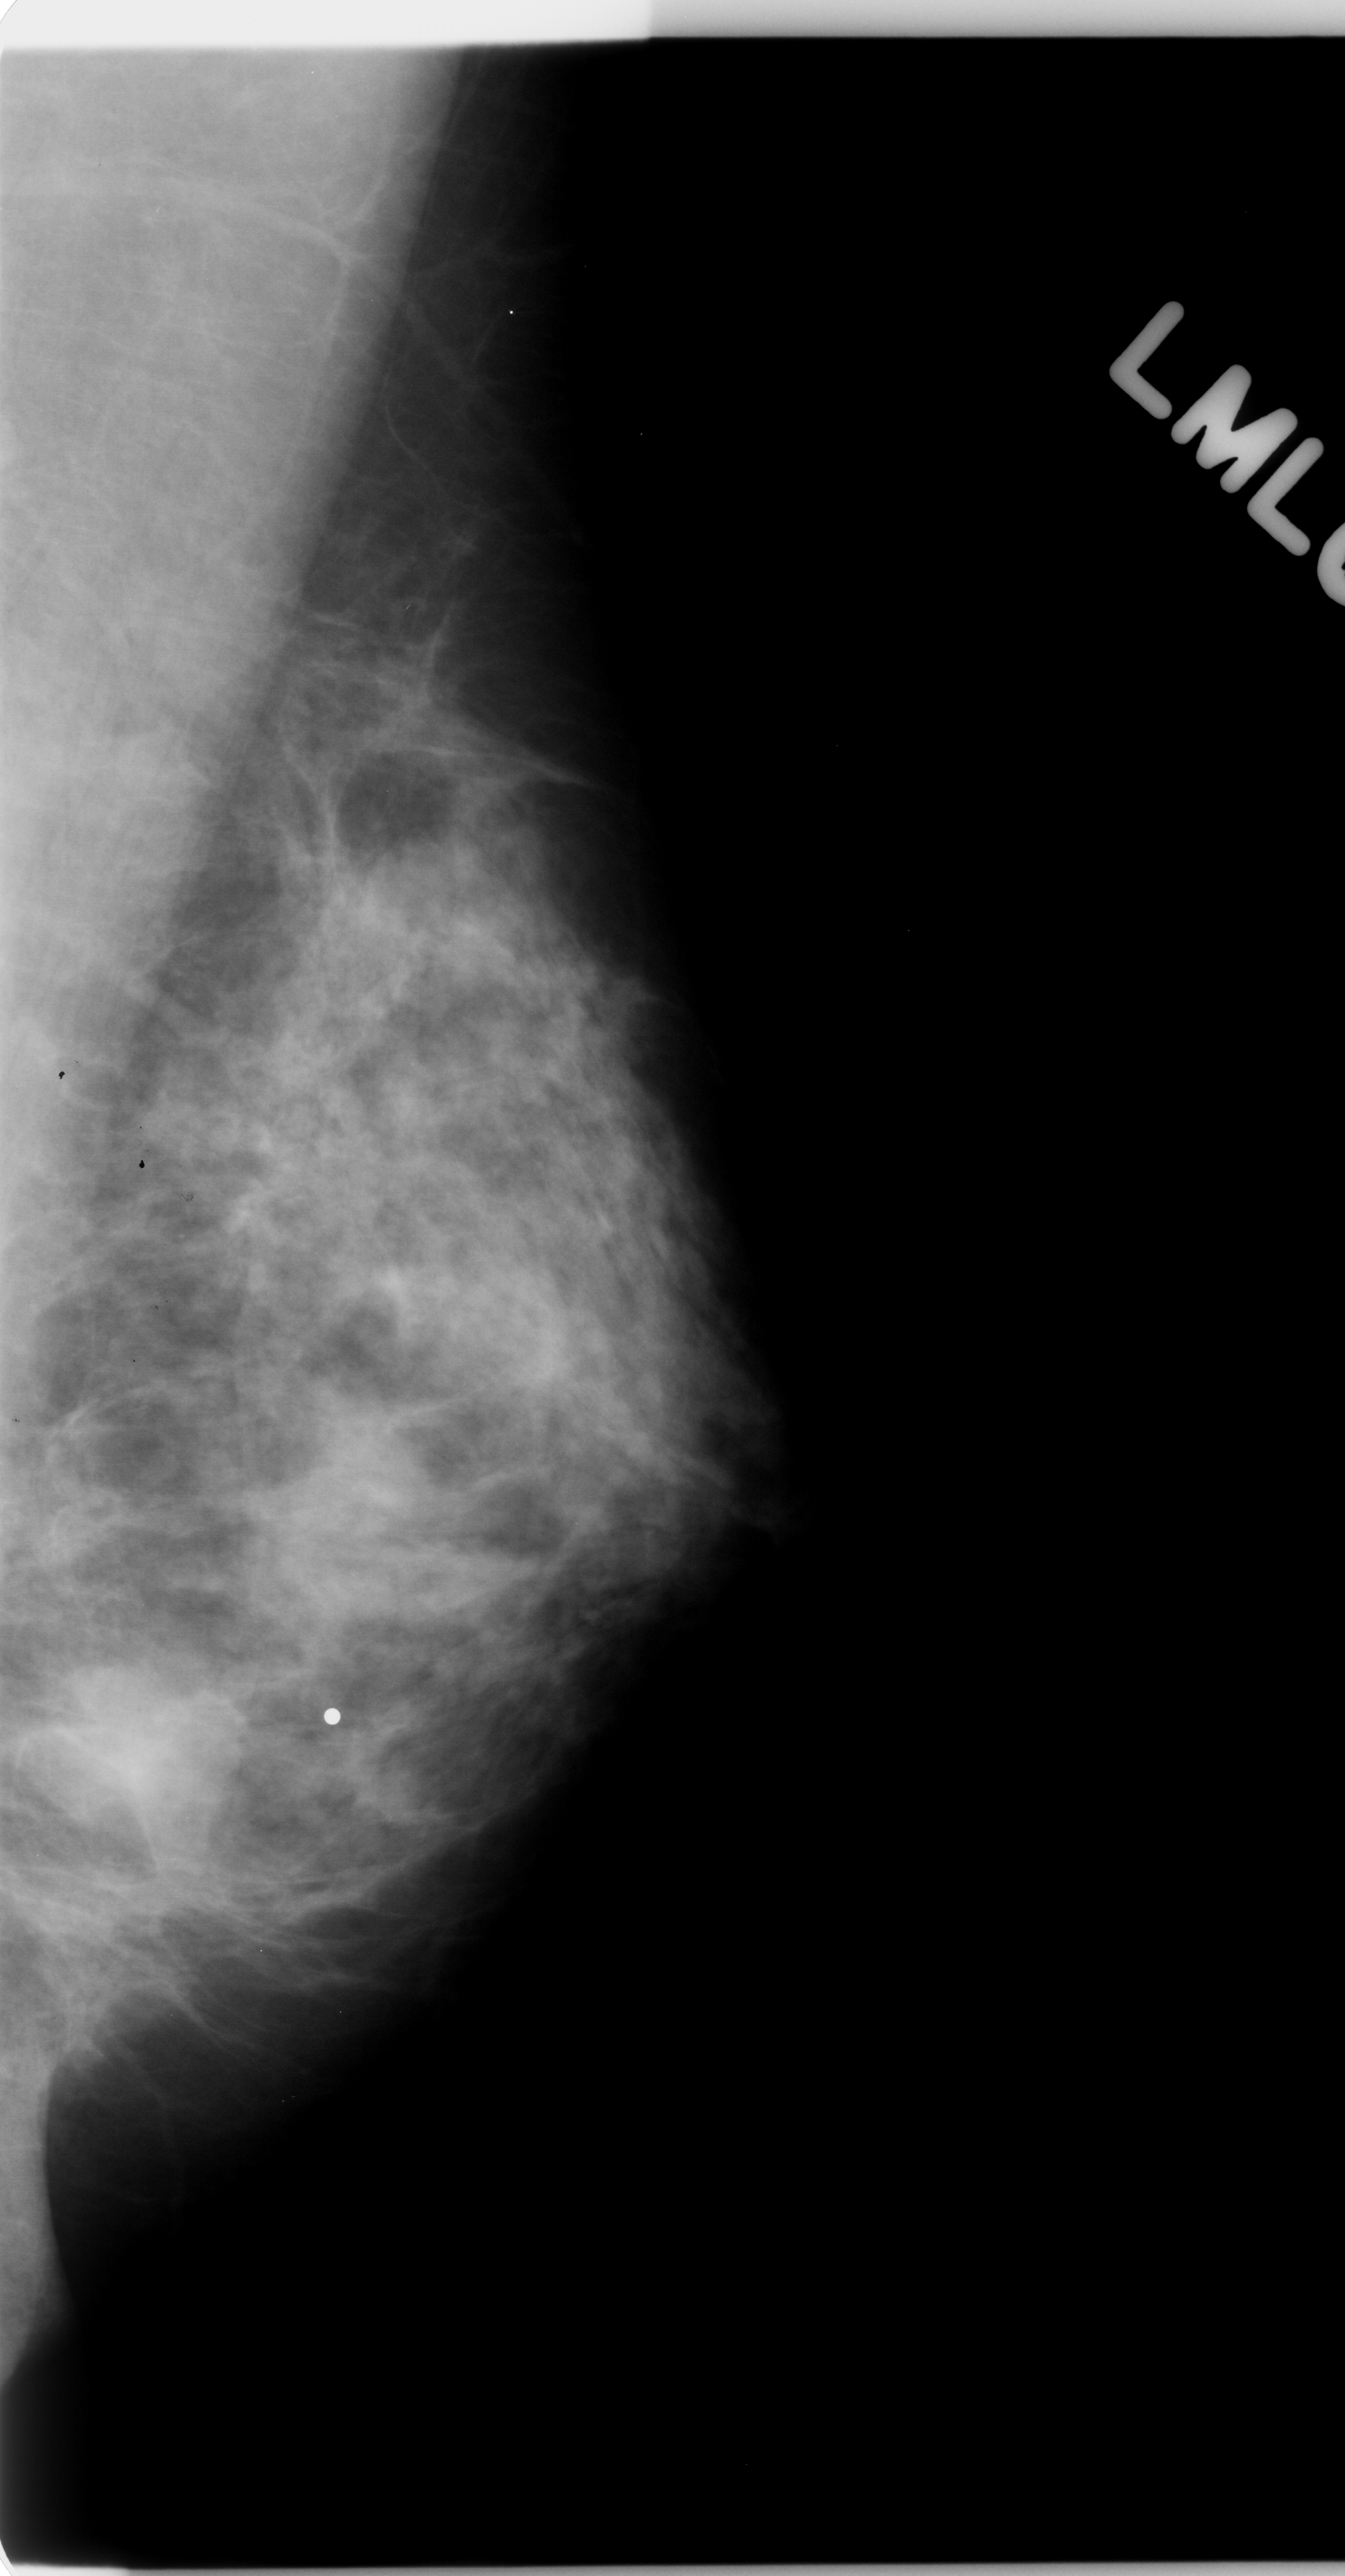
Digitized screen-film mammogram, left breast, mediolateral oblique (MLO) view, breast composition: scattered fibroglandular densities (BI-RADS density category 2 of 4).
Mass, shape lobulated, margins ill defined; BI-RADS assessment category 4; subtlety rating 4 on a 1 (subtle) to 5 (obvious) scale; pathology result (as recorded, not read from the image): malignant.